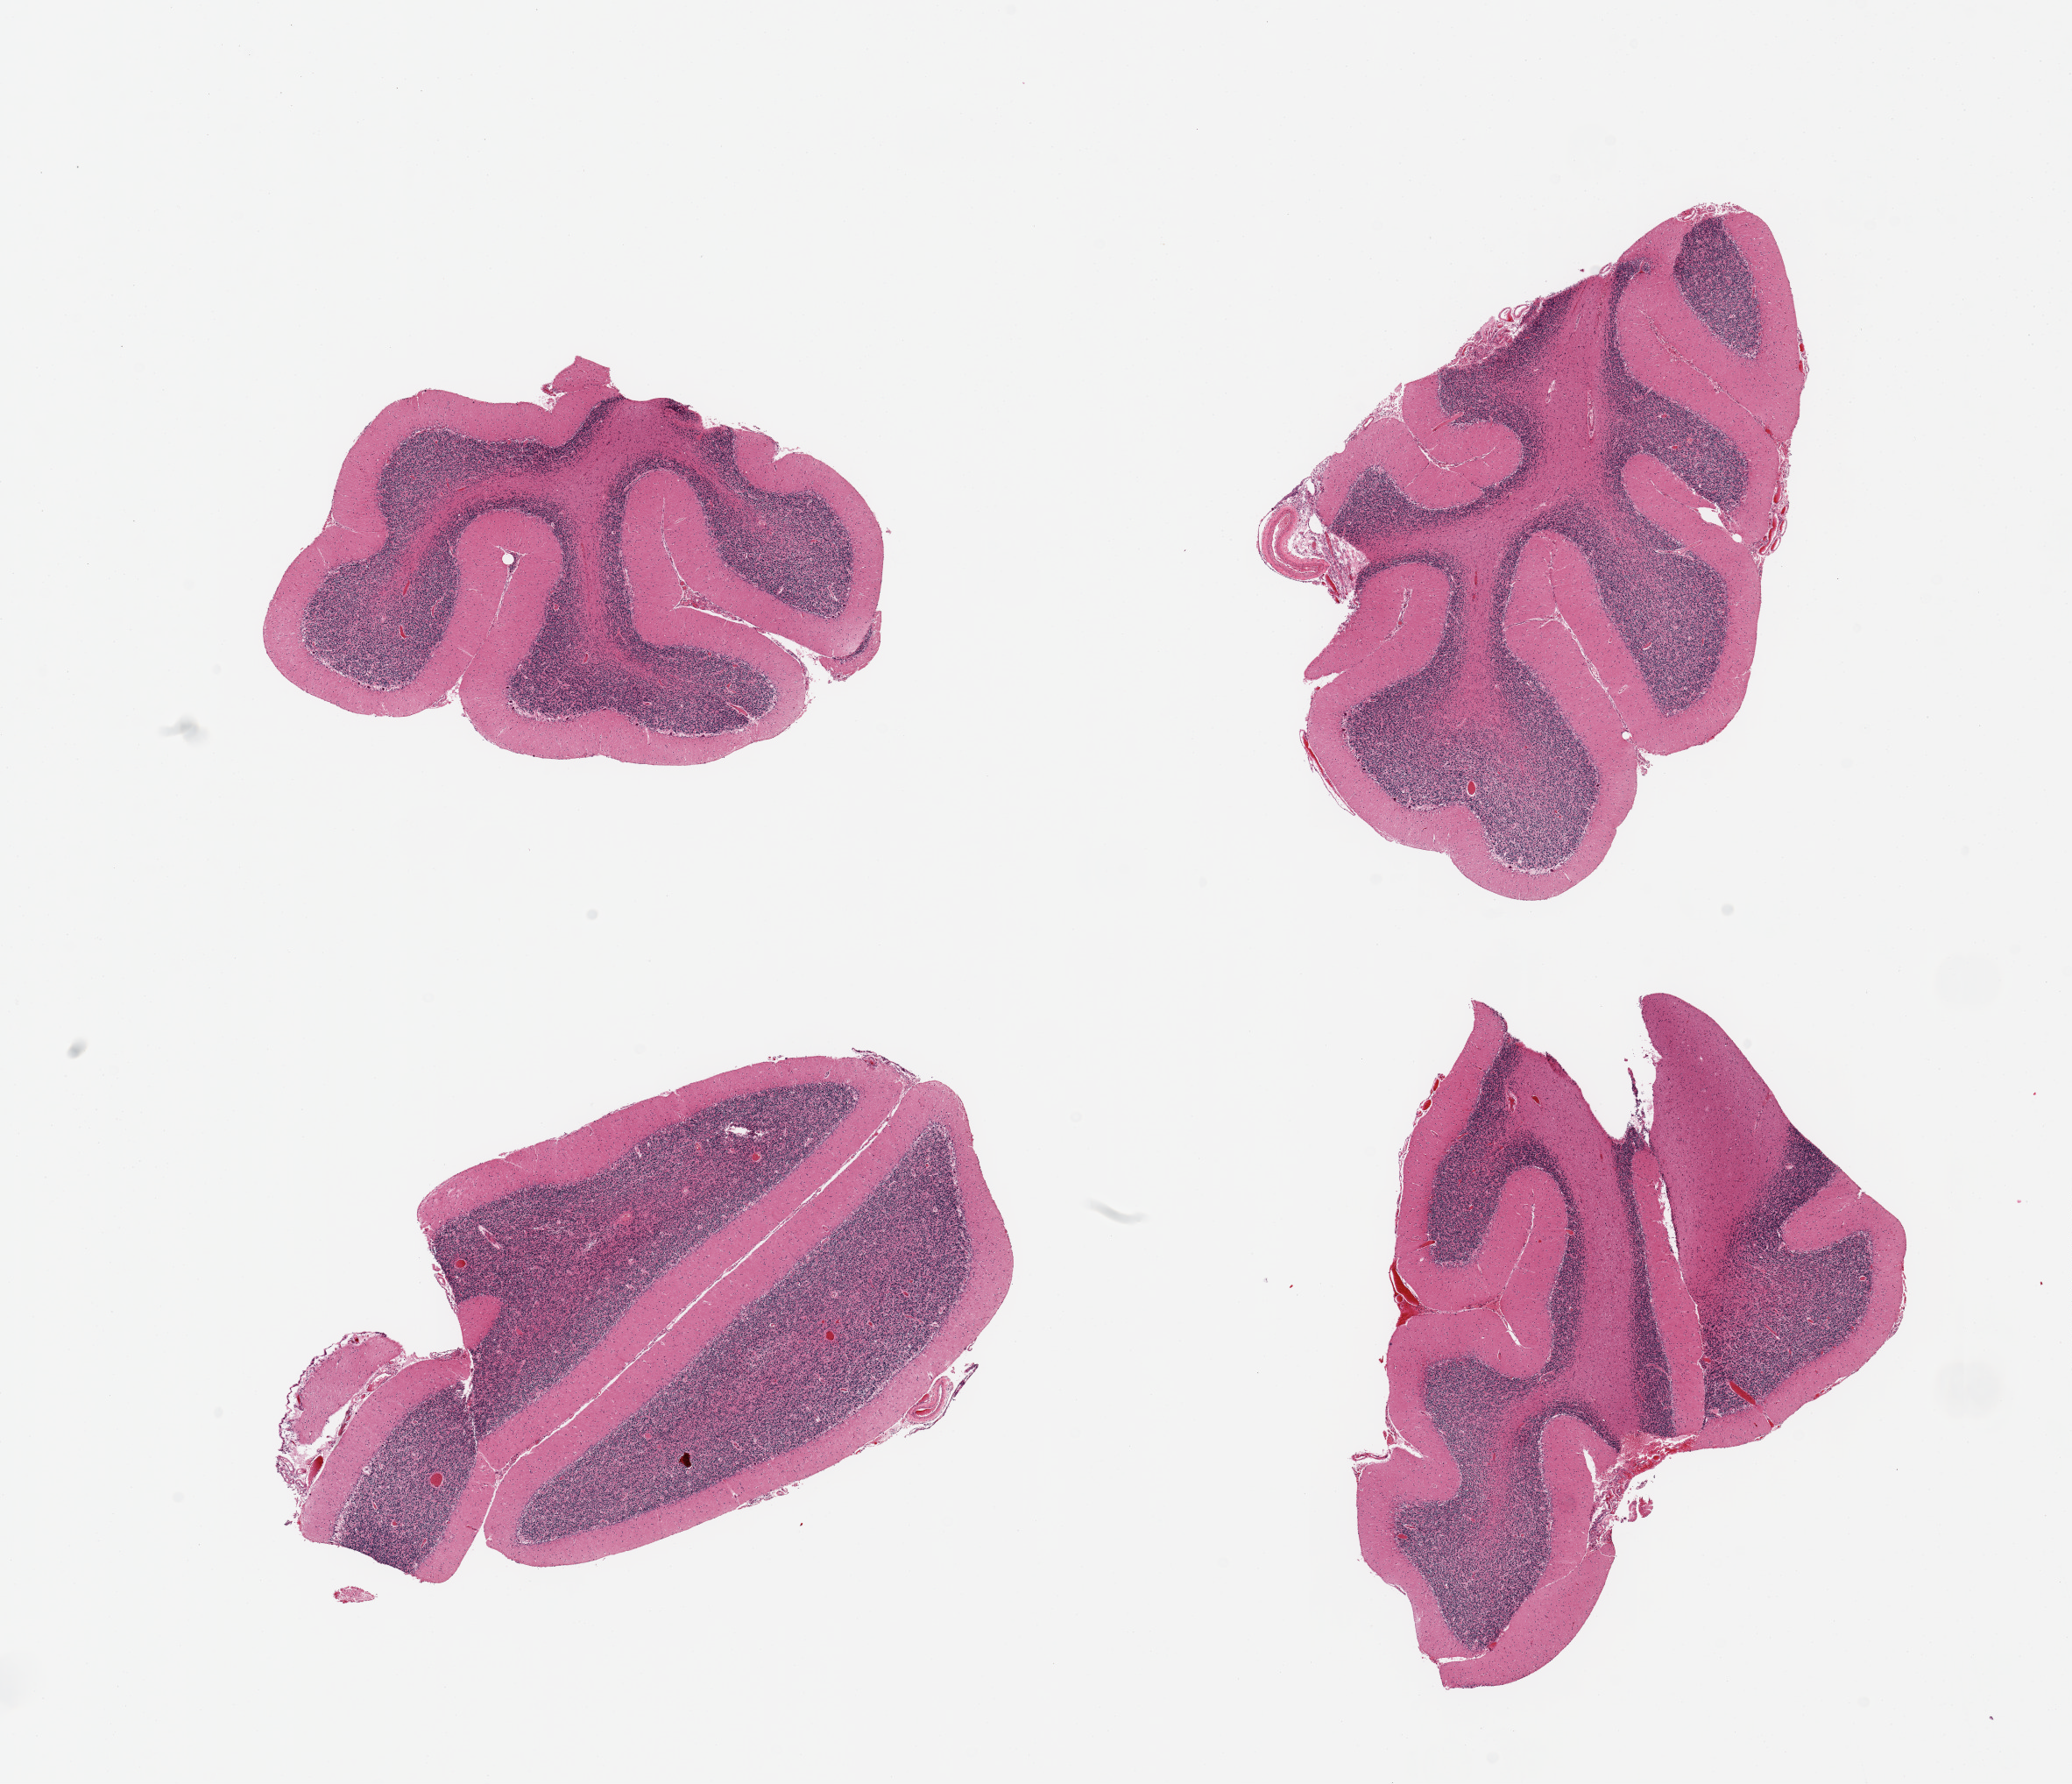
Digitized H&E-stained section, brightfield, whole scanned area (about 18.7 x 16.1 mm) shown as a low-resolution overview, PAXgene-fixed, paraffin-embedded tissue, target tissue: cerebellum, donor tissue sample. Donor: female.
Review note (as recorded): 4 pieces, no abnormalities.